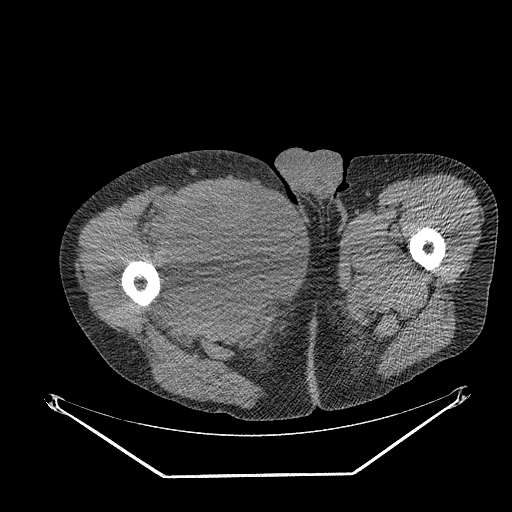
CT of an extremity soft-tissue mass (from a PET/CT study), one axial slice; position 278 of 311 along the scan axis; reconstruction kernel STANDARD; 140 kVp; soft-tissue window (W 400 / L 40 HU); 3.75 mm slice thickness; 512 × 512 image matrix. Male patient. Case-level facts recorded for this patient, not image findings: histological type: undifferentiated - pleiomorphic; grade: high; site of the primary tumour: right thigh.
Annotated regions visible in this slice (expert contour drawn on MRI and transferred to this co-registered scan by the dataset authors):
- gross tumour volume including surrounding oedema: bounding box <169,183,264,277> (left, top, right, bottom; pixels)
- gross tumour volume (mass): <169,185,263,279>